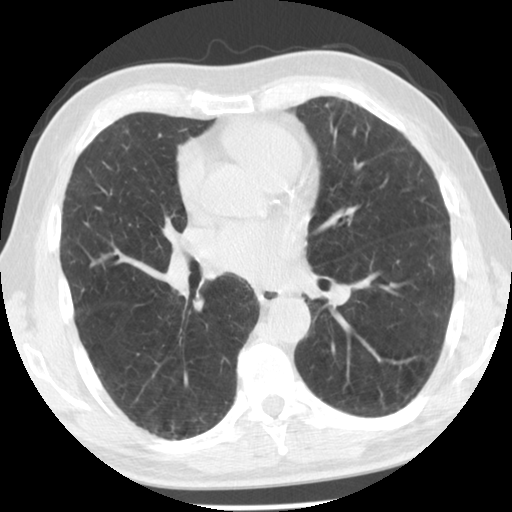
Low-dose screening chest CT, one axial slice. Slice 65 of 129 in the series (ordered by position). Reconstruction kernel STANDARD. 140 kVp. Lung window (W 1500 / L -600 HU). 2.5 mm slice thickness. 512 × 512 image matrix, field of view 330 × 330 mm.
Structures marked on this image (outlined manually by an expert reader):
- lesion 1 (tumor, upper lobe of left lung): bounding box (x1, y1, x2, y2) in pixels: (326, 104, 328, 107)